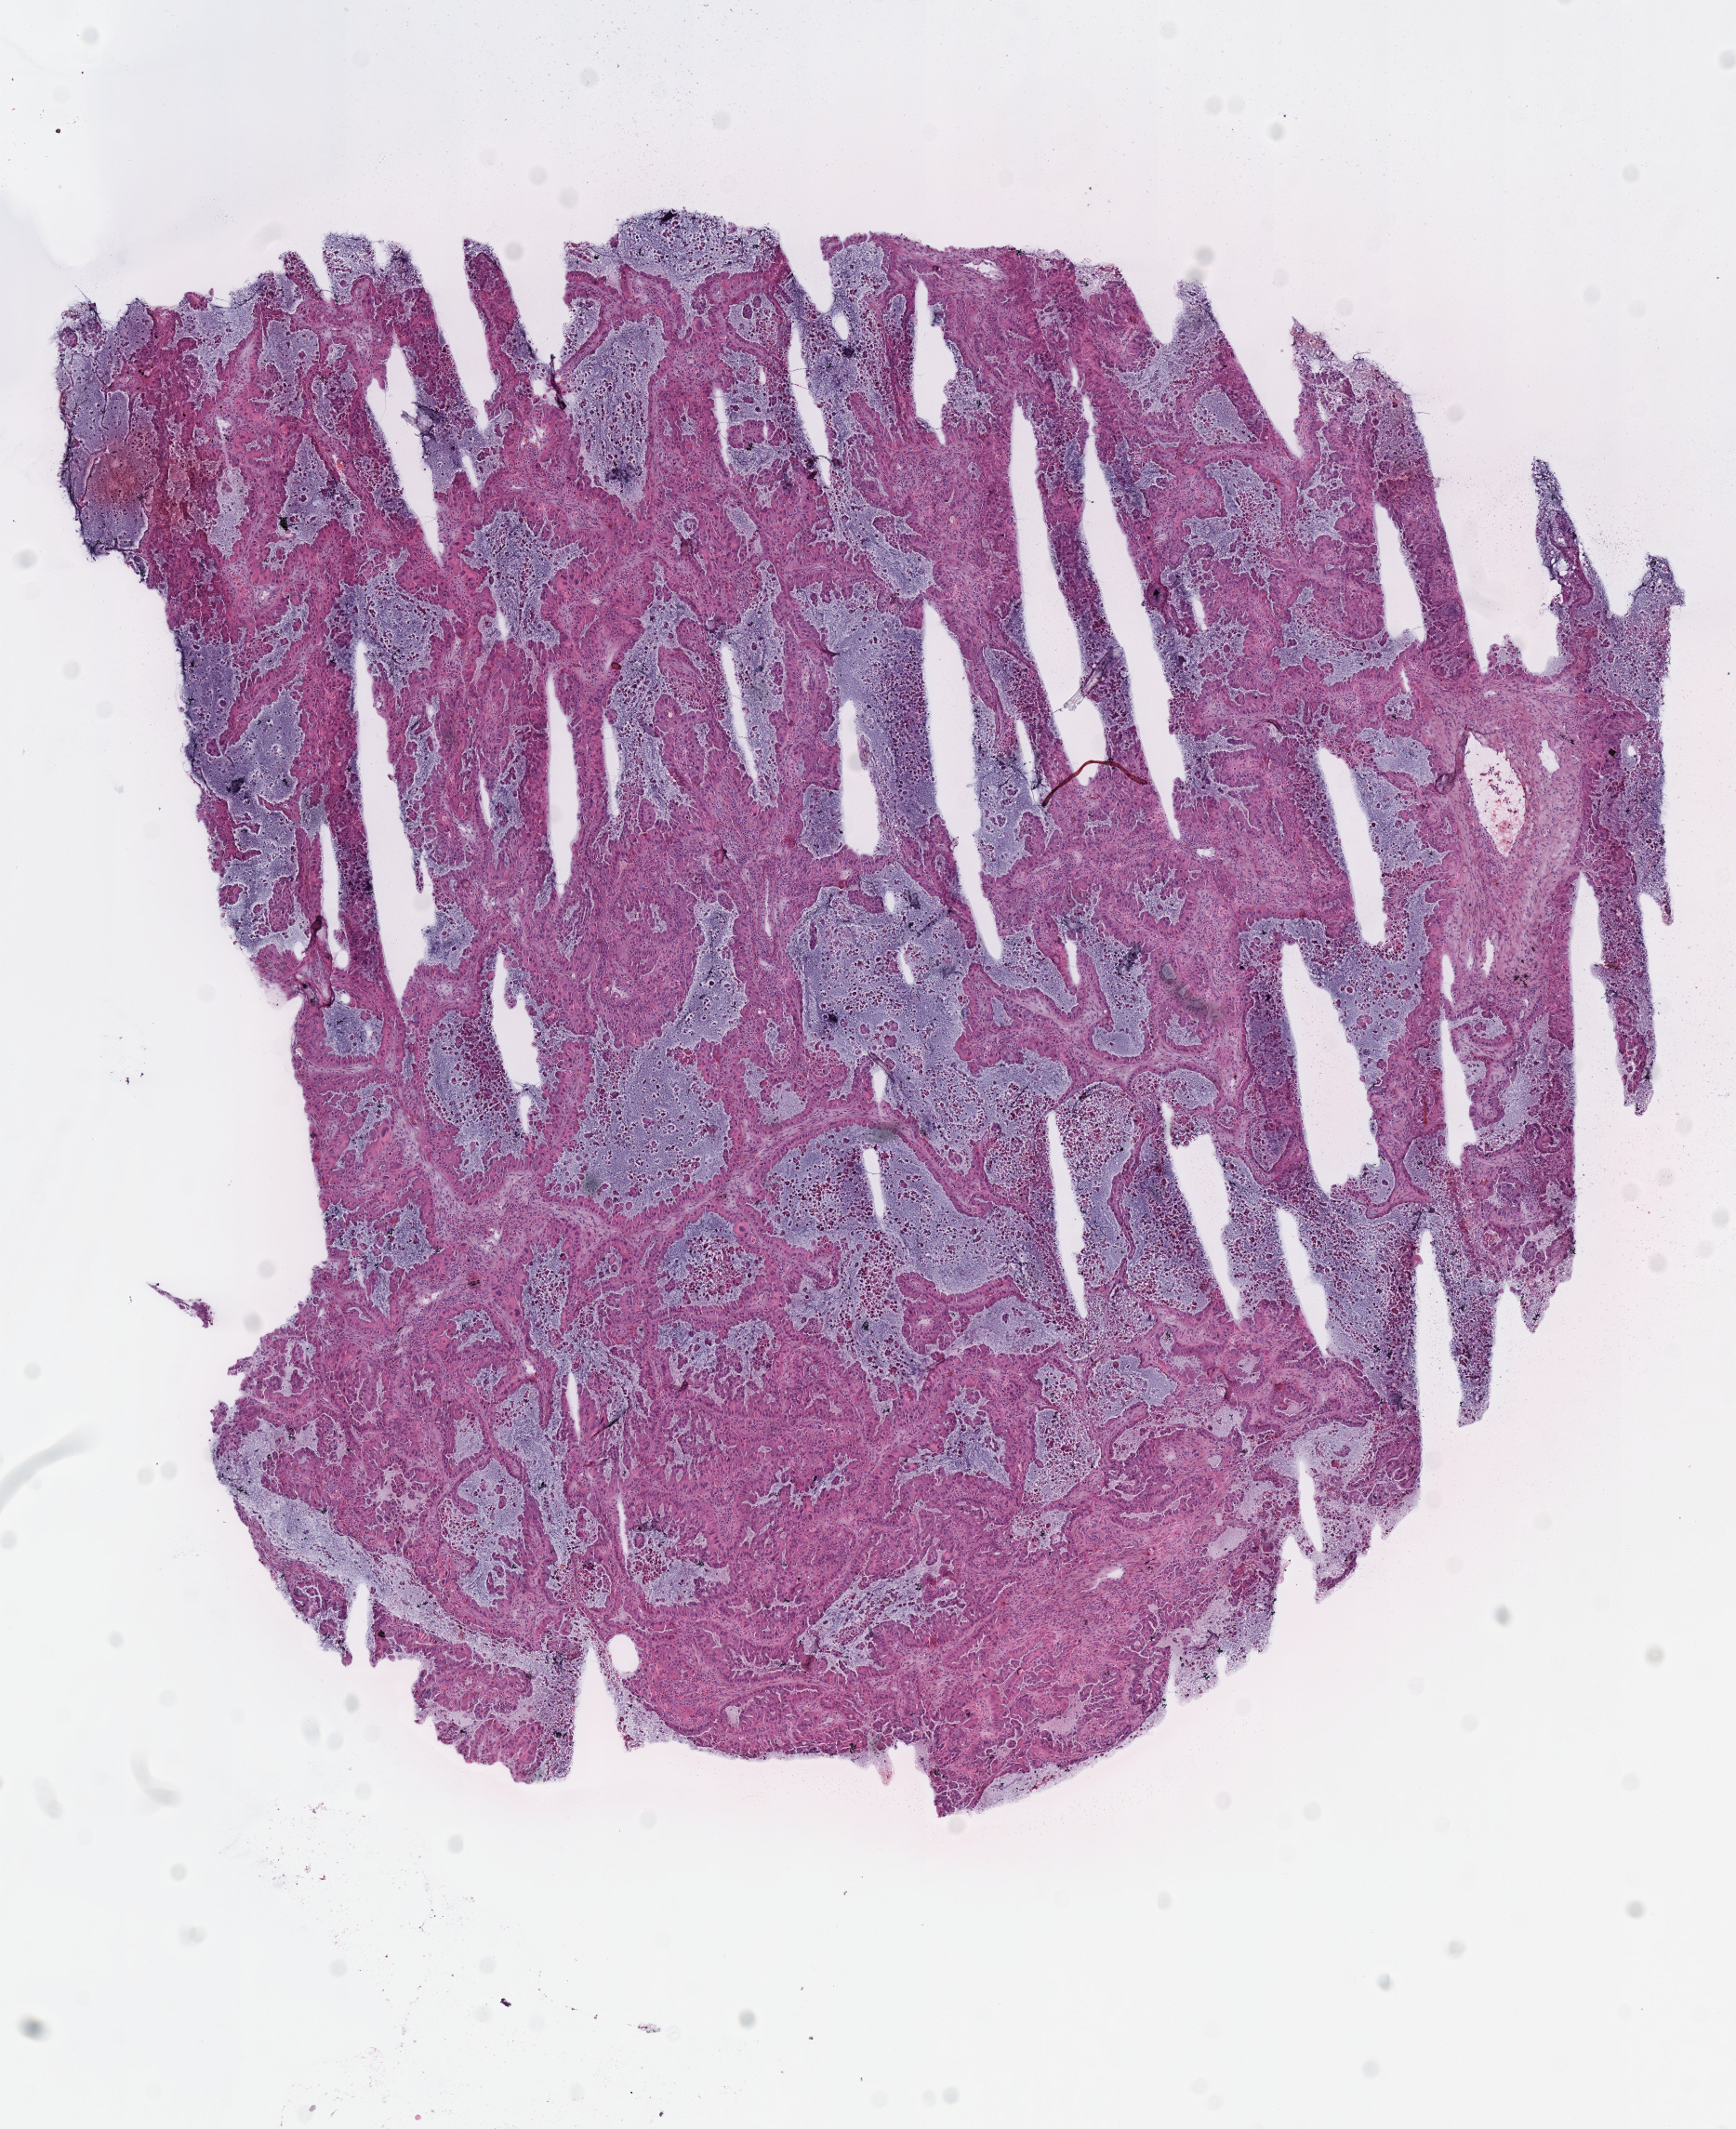
Digitized H&E tissue section (whole slide), shown as a low-resolution overview of the whole scanned area (about 7.3 x 9.0 mm); frozen section from the top of the tissue portion; primary tumour sample from the lung. Patient: male, age at initial diagnosis 55 years. Slide review estimates, as recorded: tumour cells 95%, tumour nuclei 70%, normal cells 0%, stromal cells 0%, necrosis 5%. Inflammatory infiltration, as recorded: lymphocyte infiltration 20%, monocyte infiltration 5%.
AJCC pathologic stage: IIIA. Laterality: right. Diagnosis: Adenocarcinoma with mixed subtypes (lower lobe, lung).